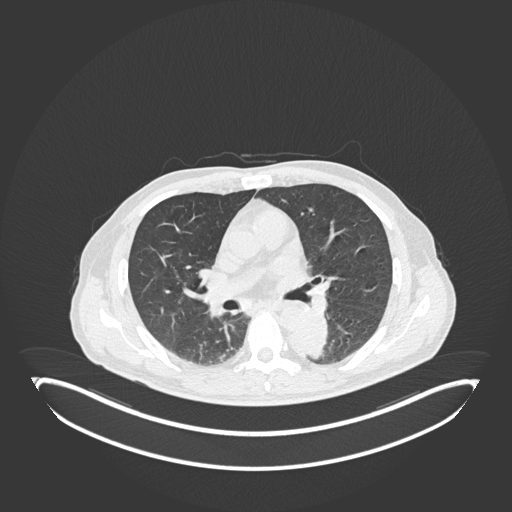
Chest CT, one axial slice; position 113 of 251 along the scan axis; 120 kVp; lung window (W 1500 / L -600 HU); 1 mm slice thickness; 512 × 512 image matrix, field of view 500 × 500 mm. Male patient, age 72 years. From the clinical record (not read from this slice): clinical TNM (as recorded): T2b N0 M1.
Outlined on this slice (rectangle marked by the reading radiologist):
- lung tumour (recorded histology: adenocarcinoma): box from (x=287, y=308) to (x=331, y=361) px